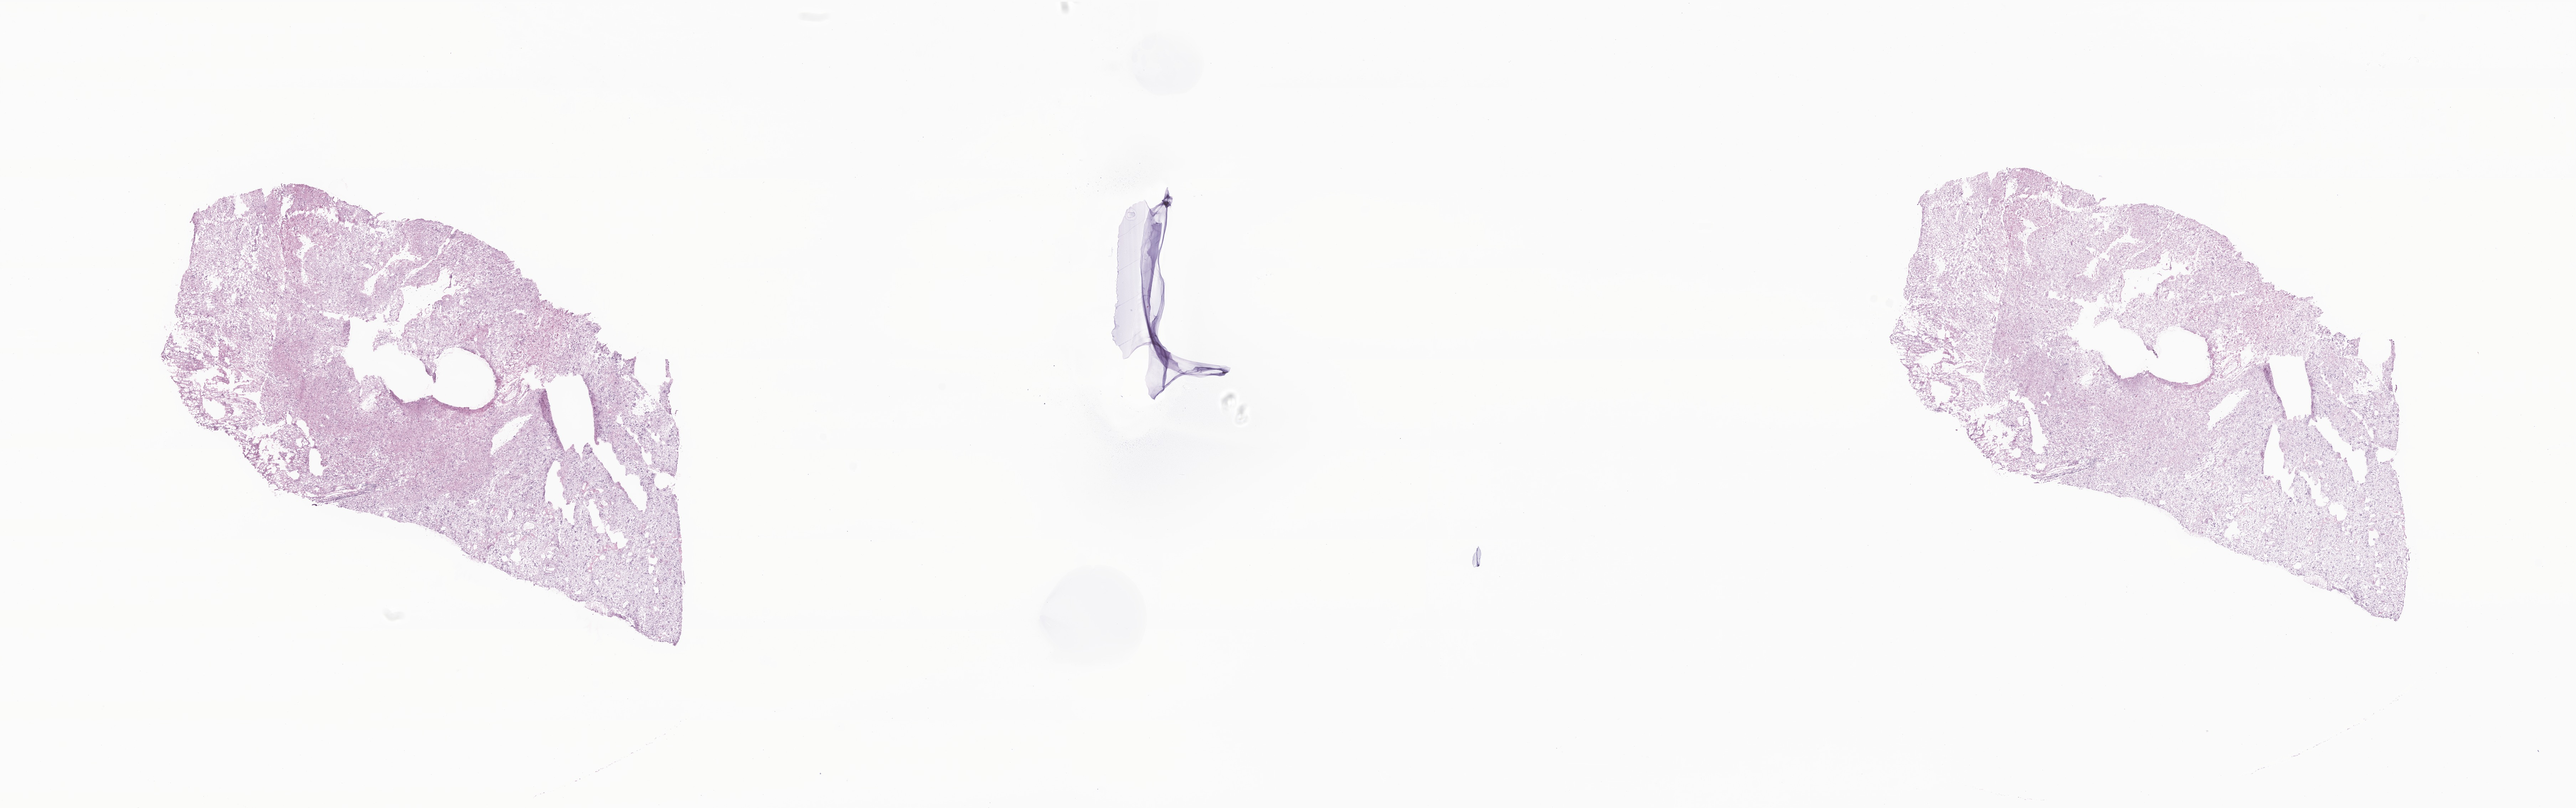
H&E whole-slide image of tumor tissue from the cerebellum, whole scanned area (about 30.5 x 9.6 mm) shown as a low-resolution overview. Frozen section. Female patient, age 179 months (14 years 11 months).
Diagnosis (ICD-O-3 morphology term): Pilocytic astrocytoma.